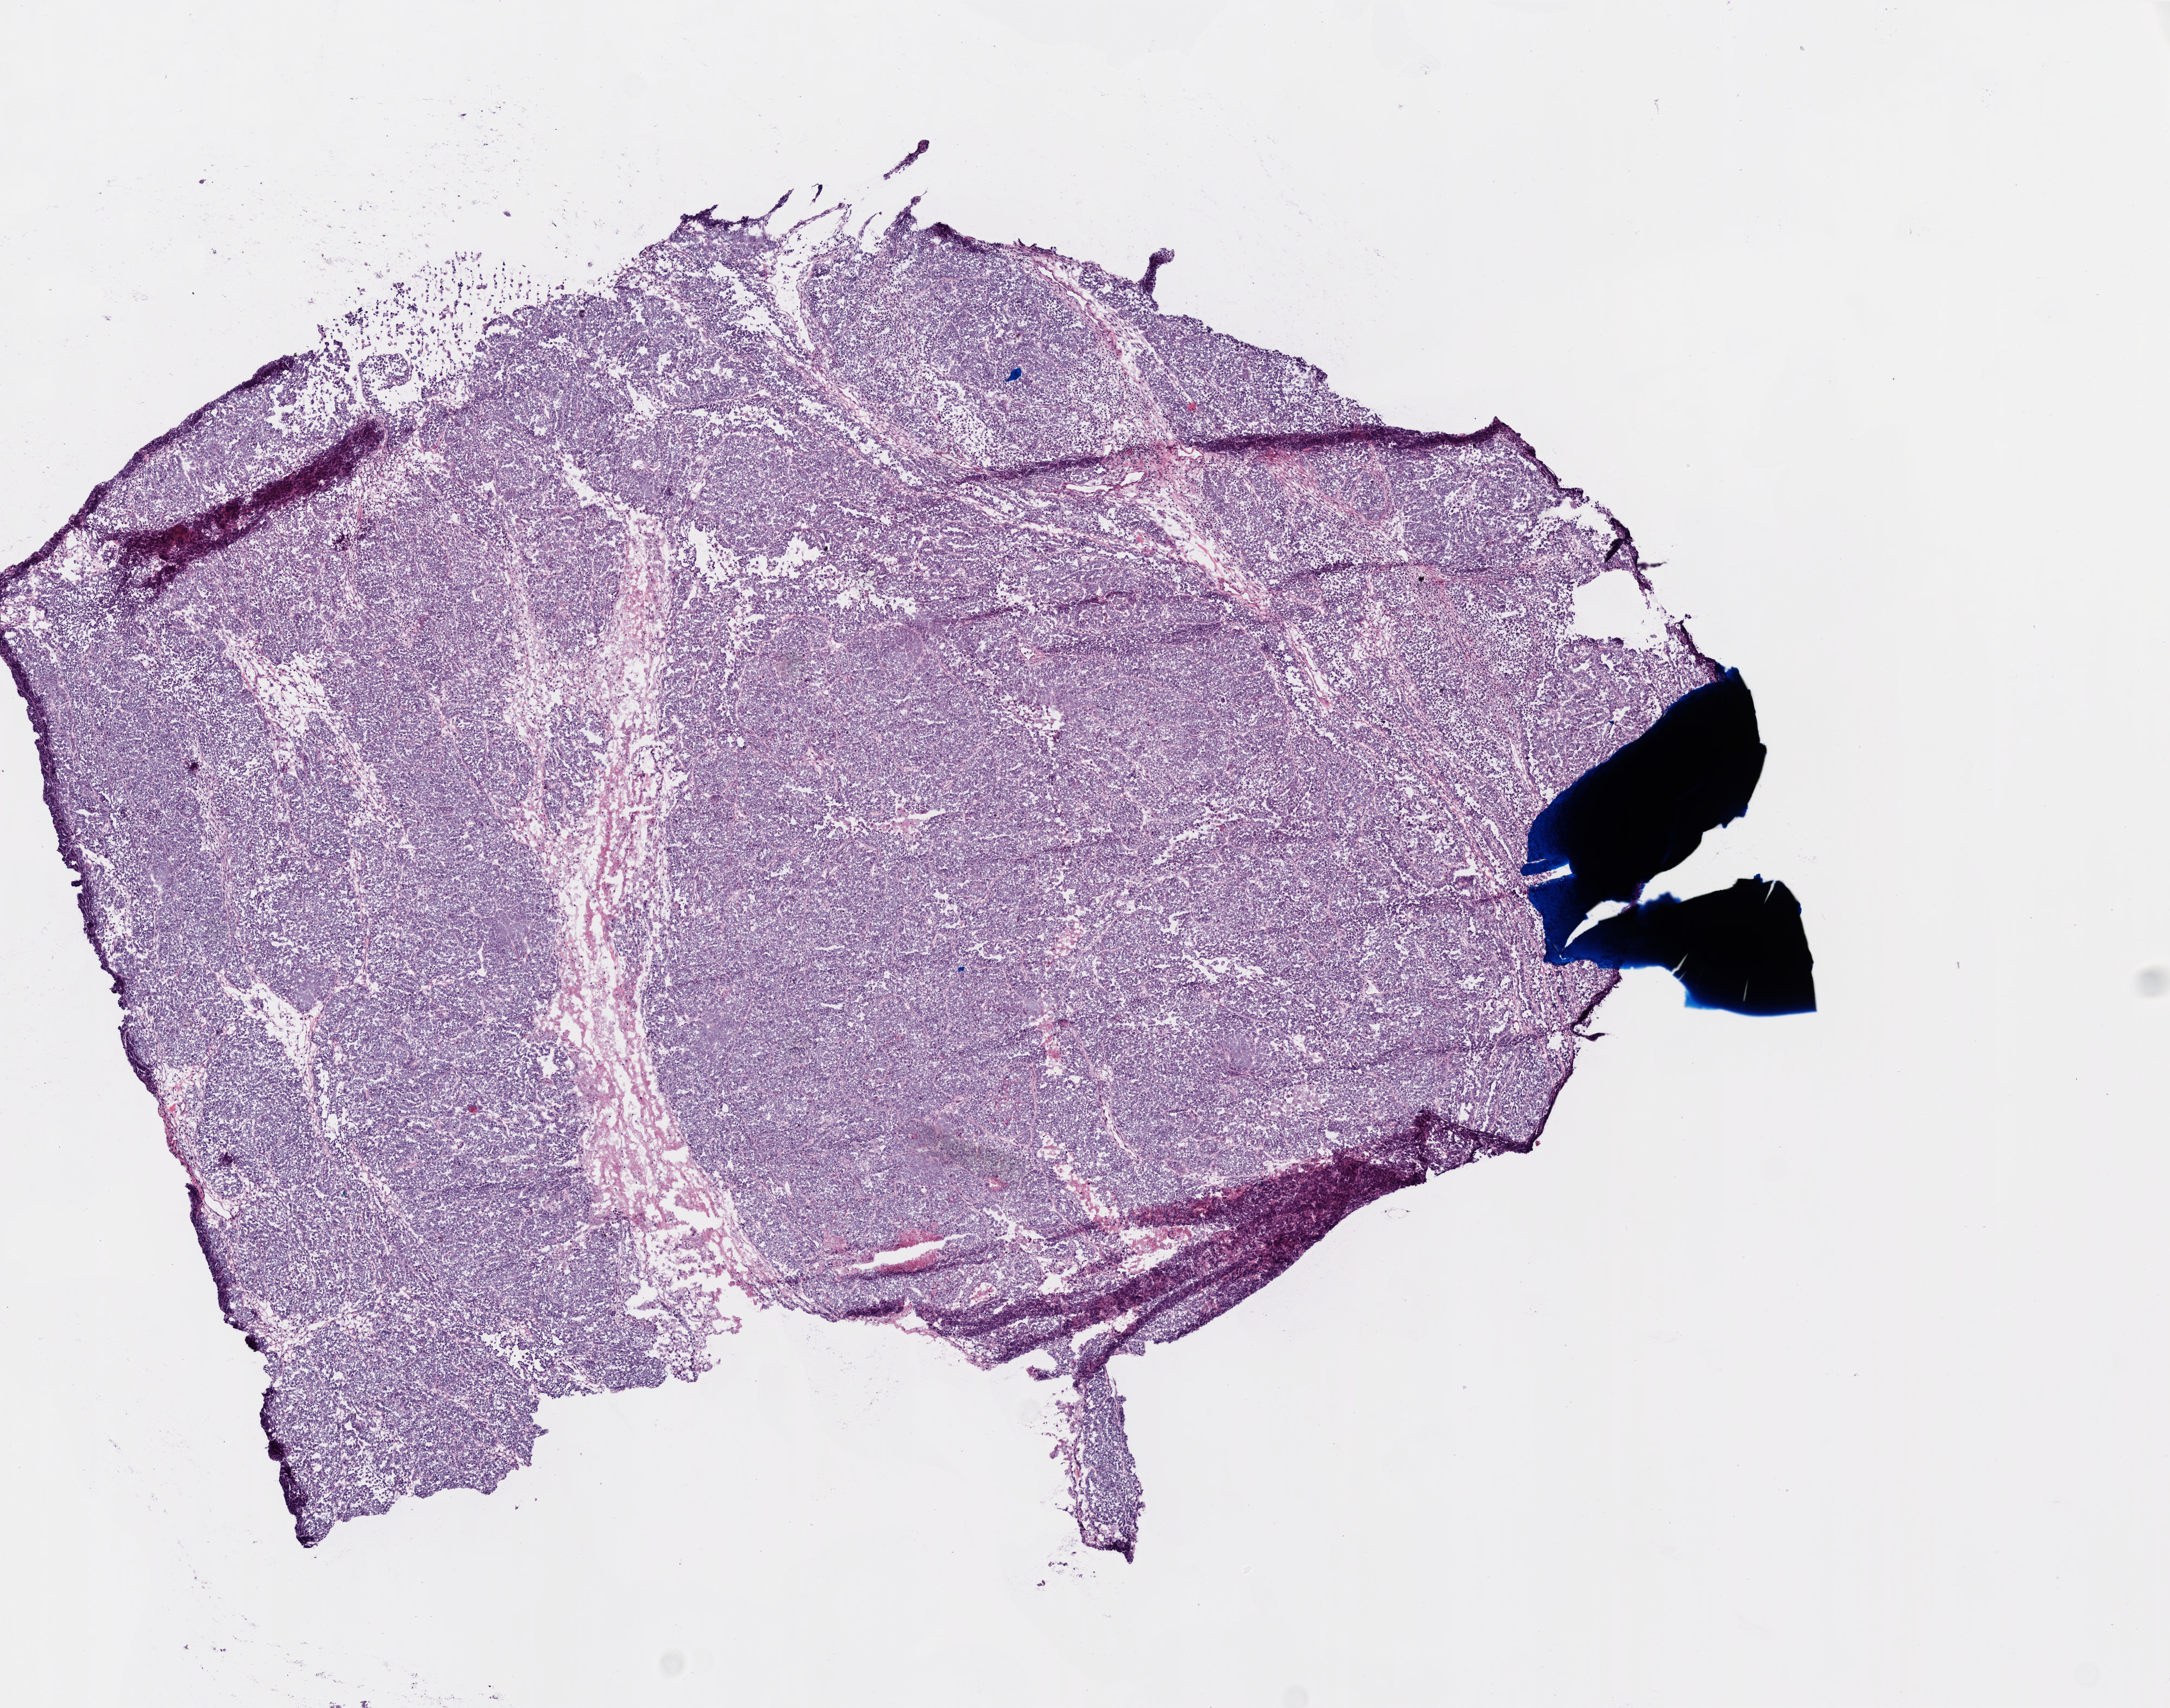
Hematoxylin and eosin (H&E) stained whole-slide image — a low-resolution overview of the entire scanned area, about 8.0 x 6.3 mm (acquisition: 20x scan); frozen section from the top of the tissue portion; primary tumour sample from the ovary. Patient: female, age at initial diagnosis 59 years. Histologic grade: G3 (poorly differentiated). Composition of this section per pathologist review: tumour cells 0%, tumour nuclei 95%, normal cells 0%, stromal cells 0%, necrosis 0%.
Histologic diagnosis: Serous cystadenocarcinoma, NOS. FIGO stage: IIIC.